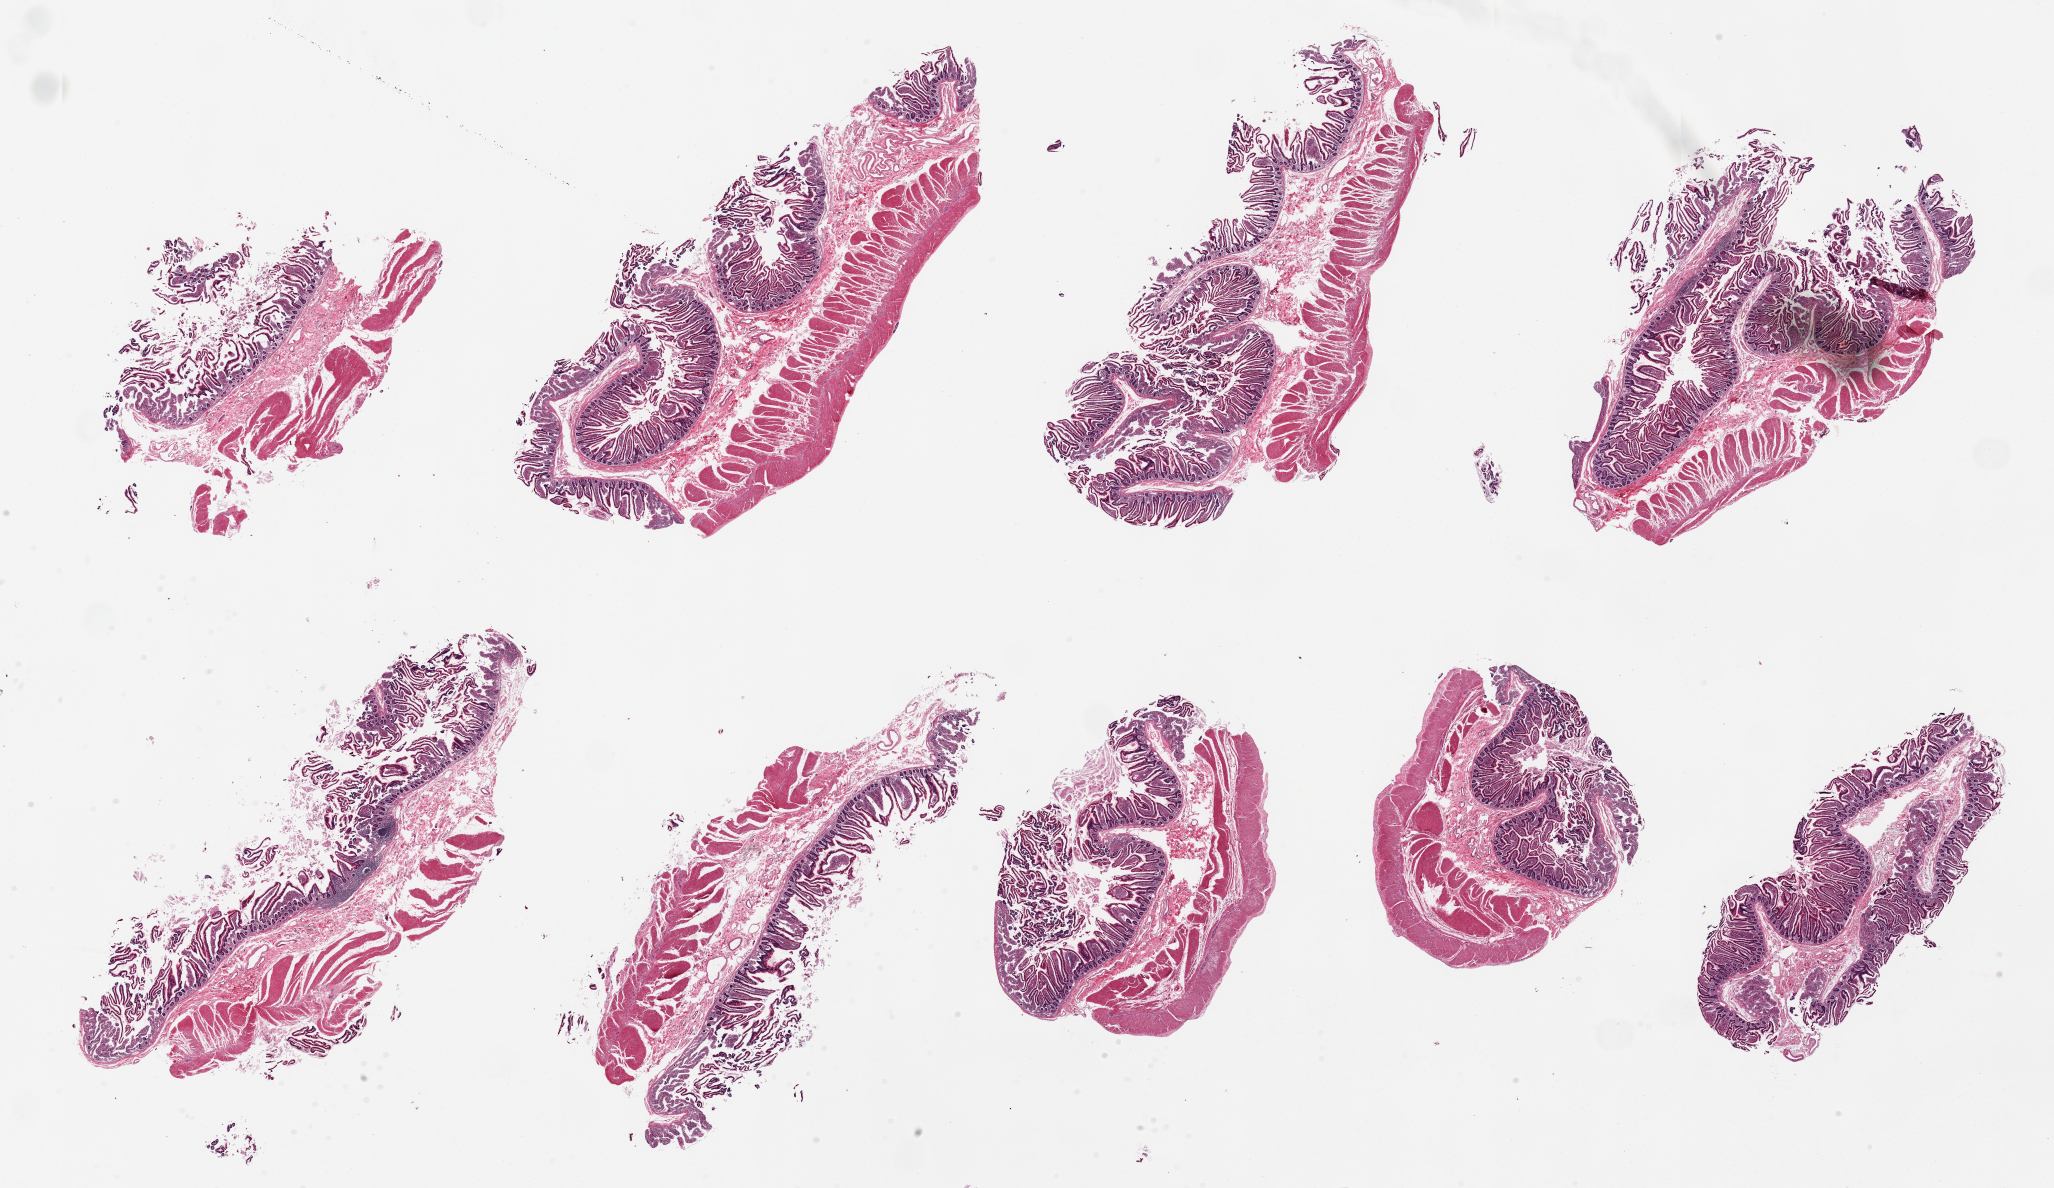
H&E whole-slide image, low-resolution overview of the scanned area, about 32.5 x 18.8 mm. PAXgene-fixed, paraffin-embedded tissue. Section of transverse colon (target tissue). Tissue donor sample. Female donor.
* reviewer comment on this tissue sample: 1 piece. 7x3.5mm; small intestine not colon